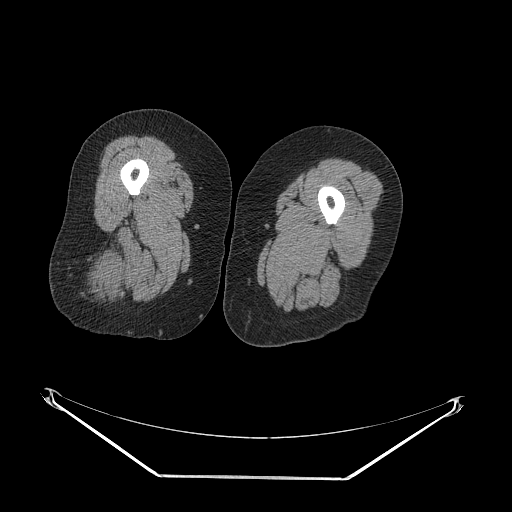
CT of an extremity soft-tissue mass (from a PET/CT study), one axial slice; position 26 of 257 along the scan axis; reconstruction kernel STANDARD; soft-tissue window (W 400 / L 40 HU); 512 × 512 image matrix, field of view 500 × 500 mm. Female patient. Case-level facts recorded for this patient, not image findings: histological type: synovial sarcoma; grade: intermediate; site of the primary tumour: right buttock.
Outlined on this slice (expert contour drawn on MRI and transferred to this co-registered scan by the dataset authors):
- gross tumour volume including surrounding oedema: bounding box <94,242,124,296> (left, top, right, bottom; pixels)
- gross tumour volume (mass): <100,260,118,275>